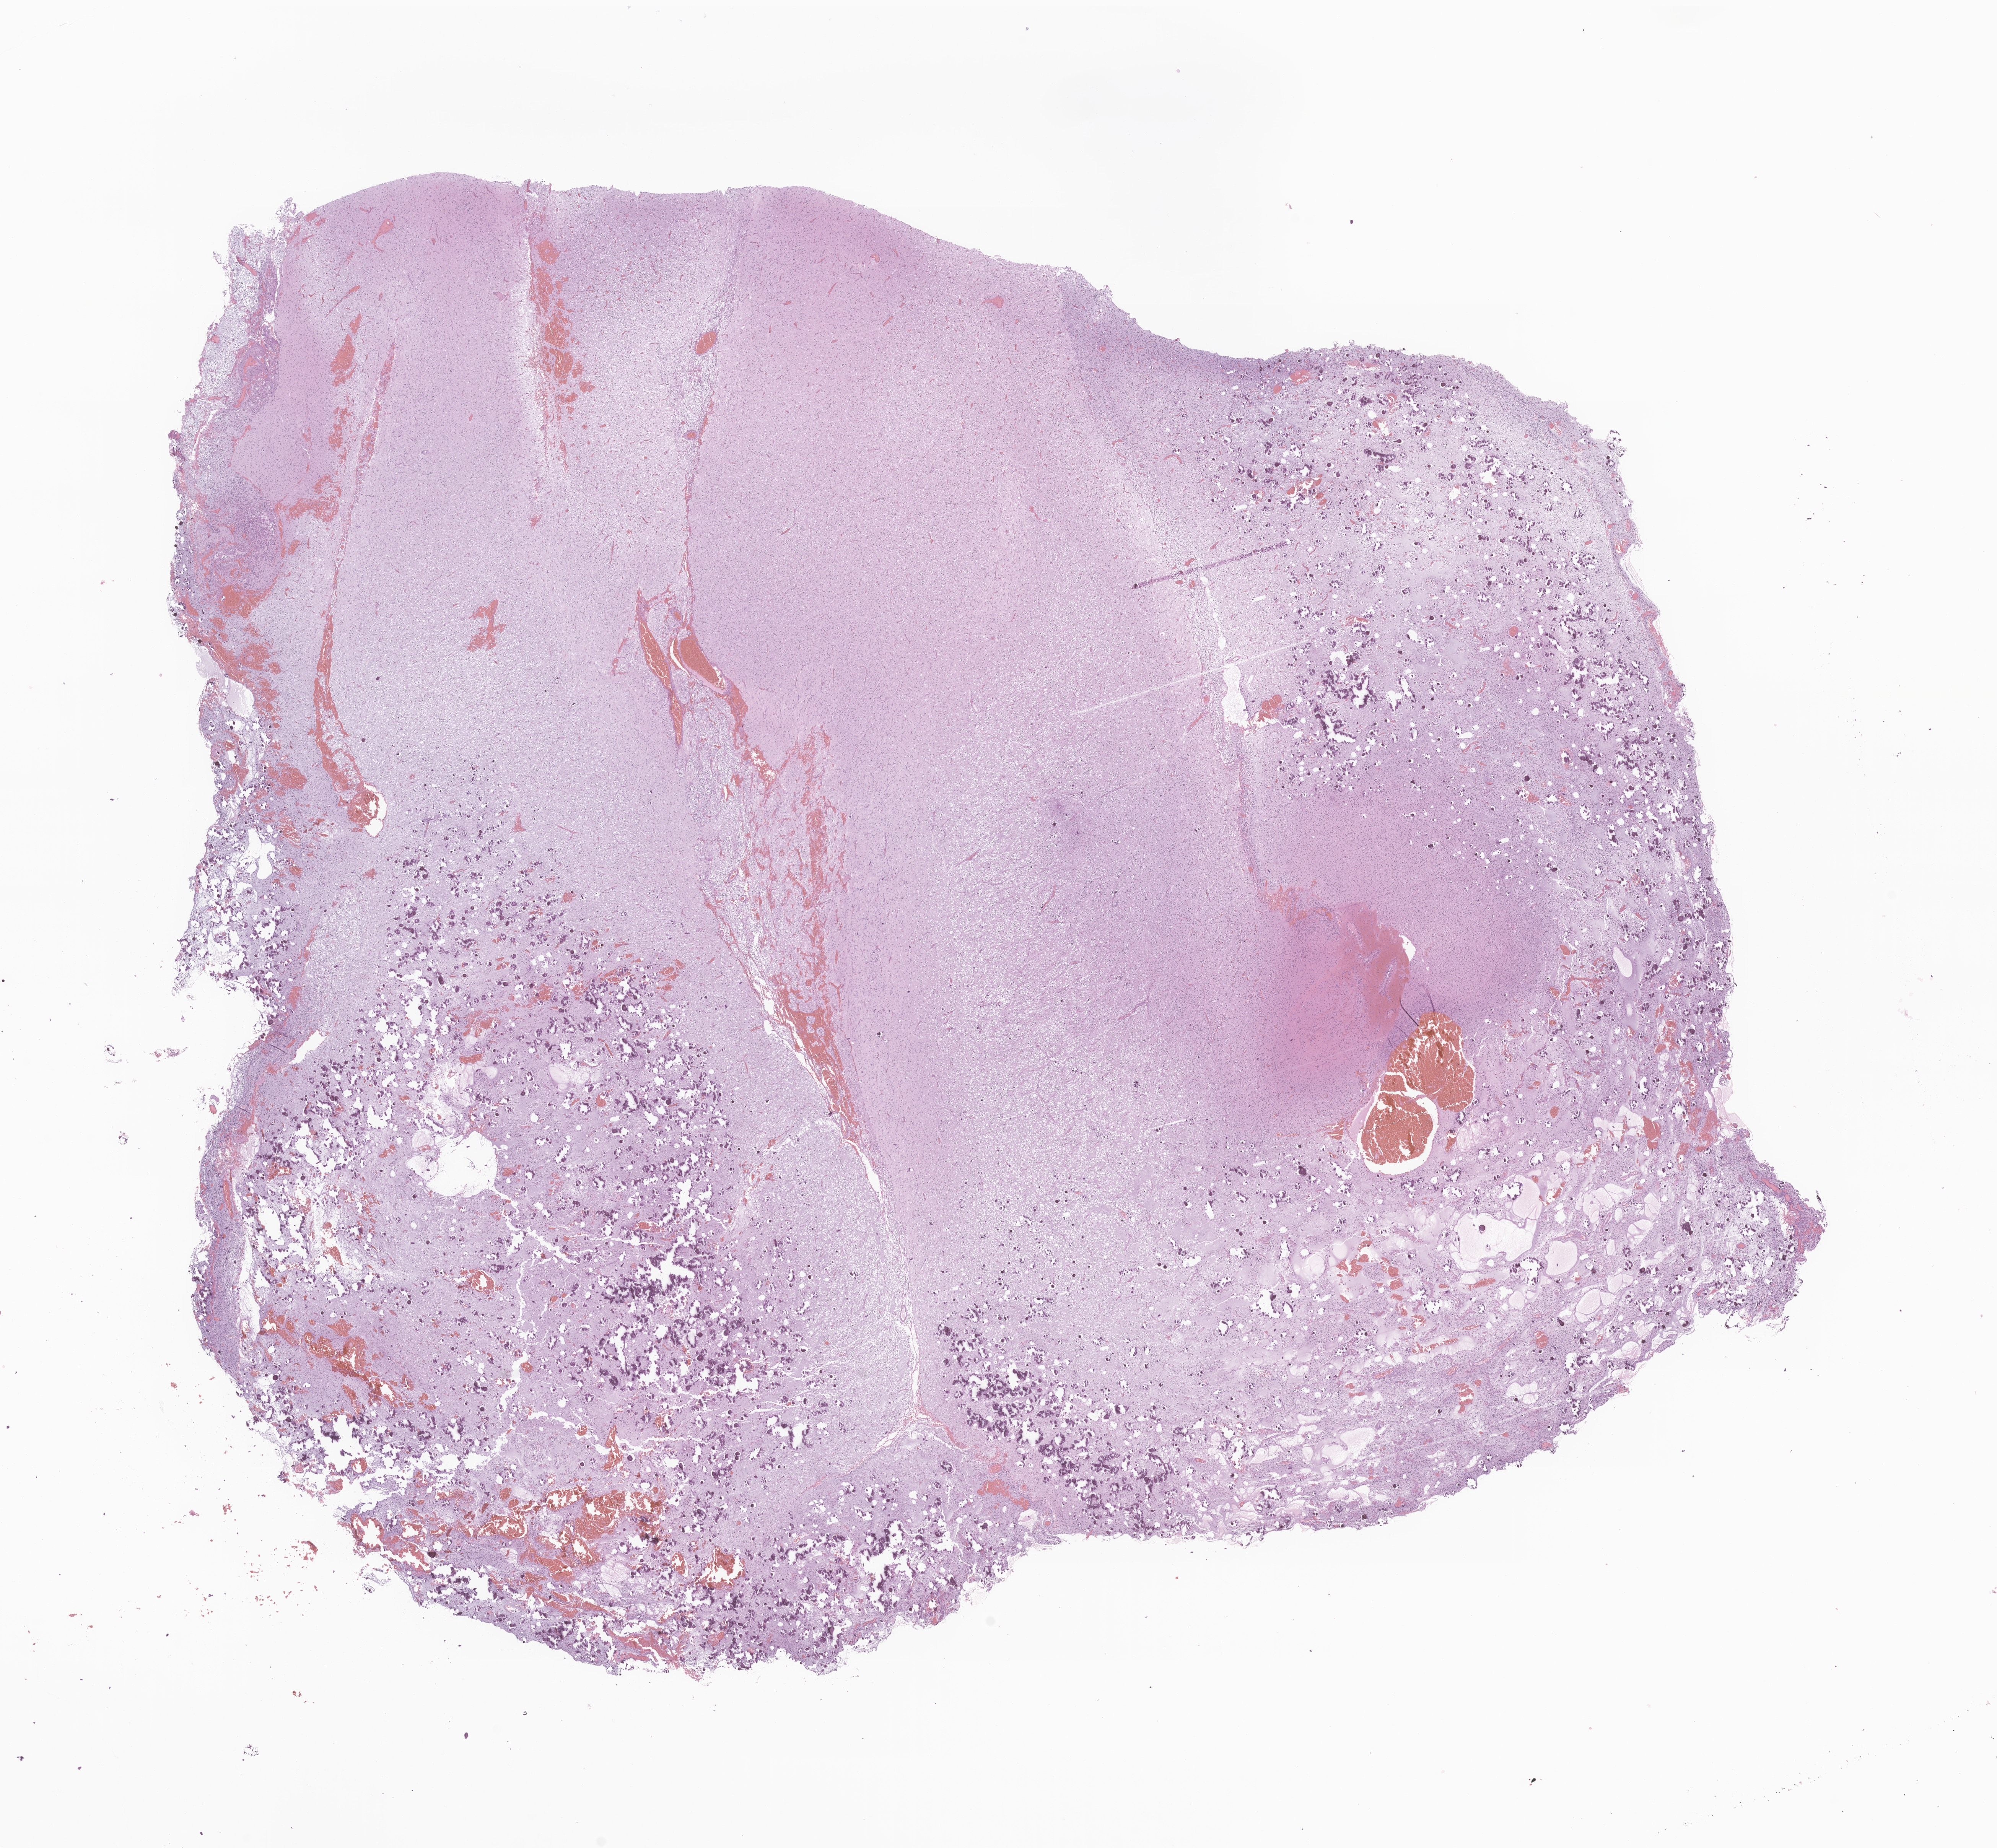
Digitized hematoxylin and eosin (H&E)-stained section of tumor tissue from the cerebellum — shown as a low-resolution overview of the whole scanned area (about 22.0 x 20.4 mm); FFPE section. Male patient, age 61 months (5 years 1 month).
Diagnosis: Glioma, malignant.